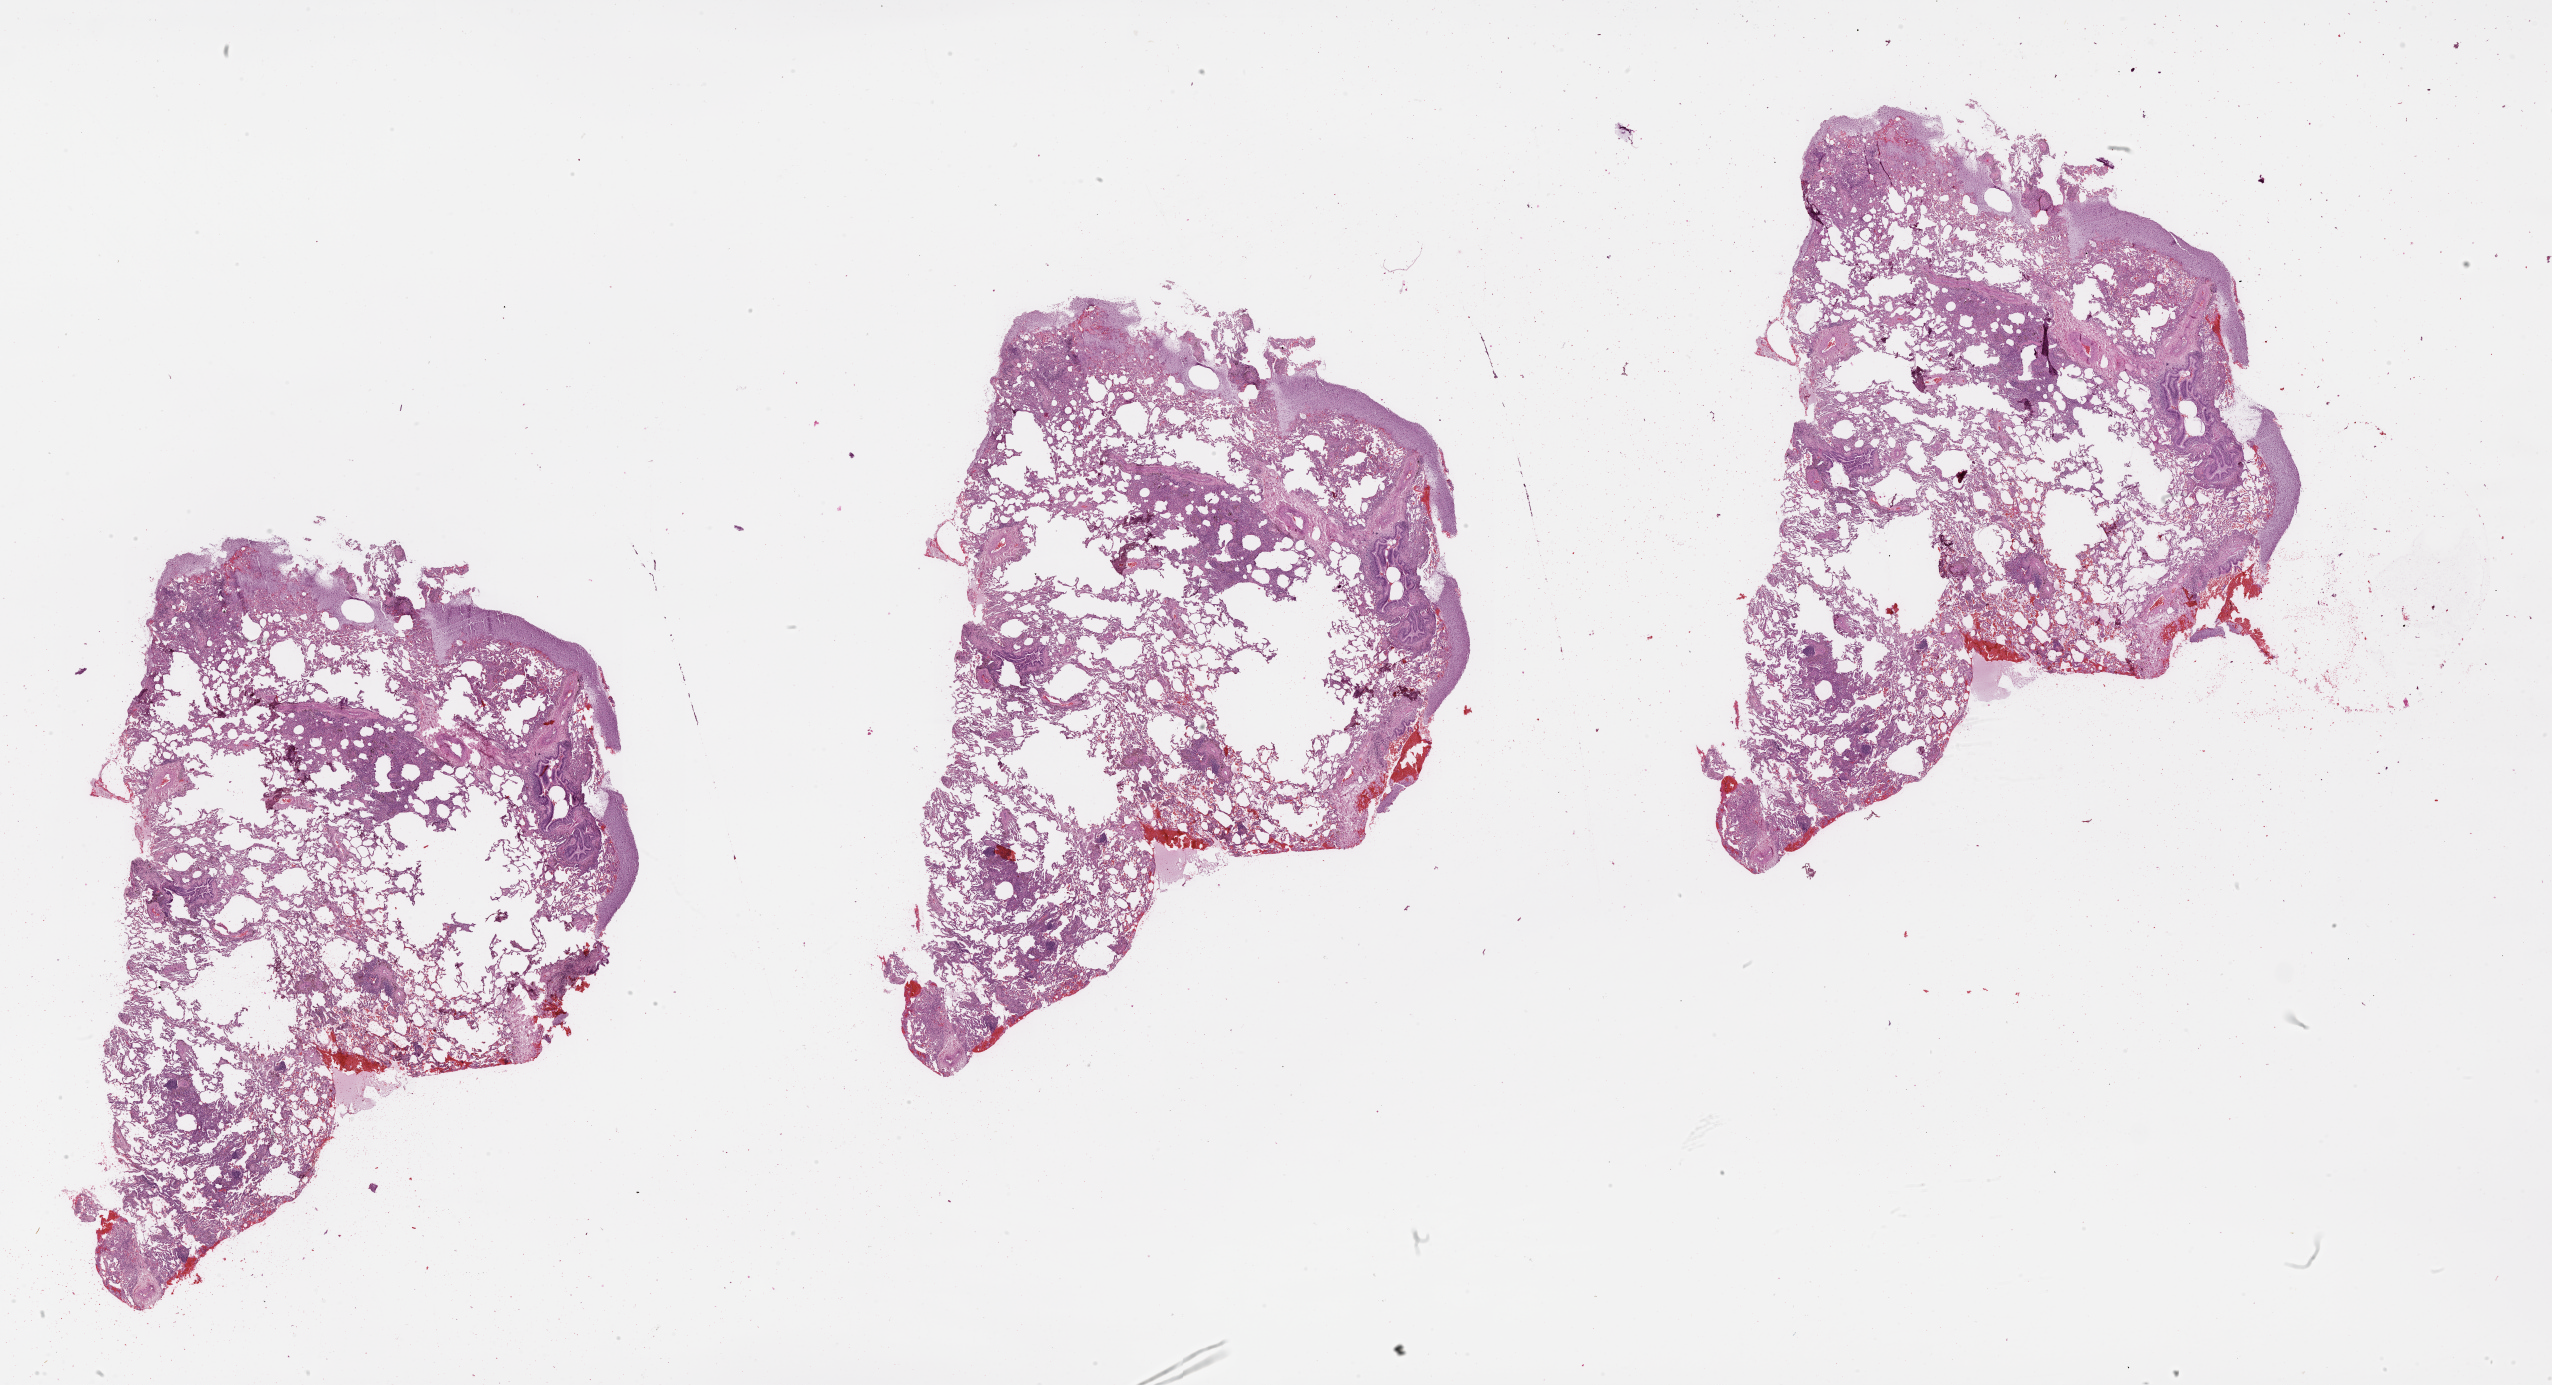
Digitized Hematoxylin and eosin (H&E) stained tissue section (whole slide), whole scanned area (about 41.1 x 22.3 mm, slide scanned at 20x) shown as a low-resolution overview. Lung, normal (non-tumour) tissue. Patient: male, age 43 years.
- this section: normal (non-tumour) tissue from the same patient
- patient diagnosis (cohort enrolment): squamous cell carcinoma (lung)